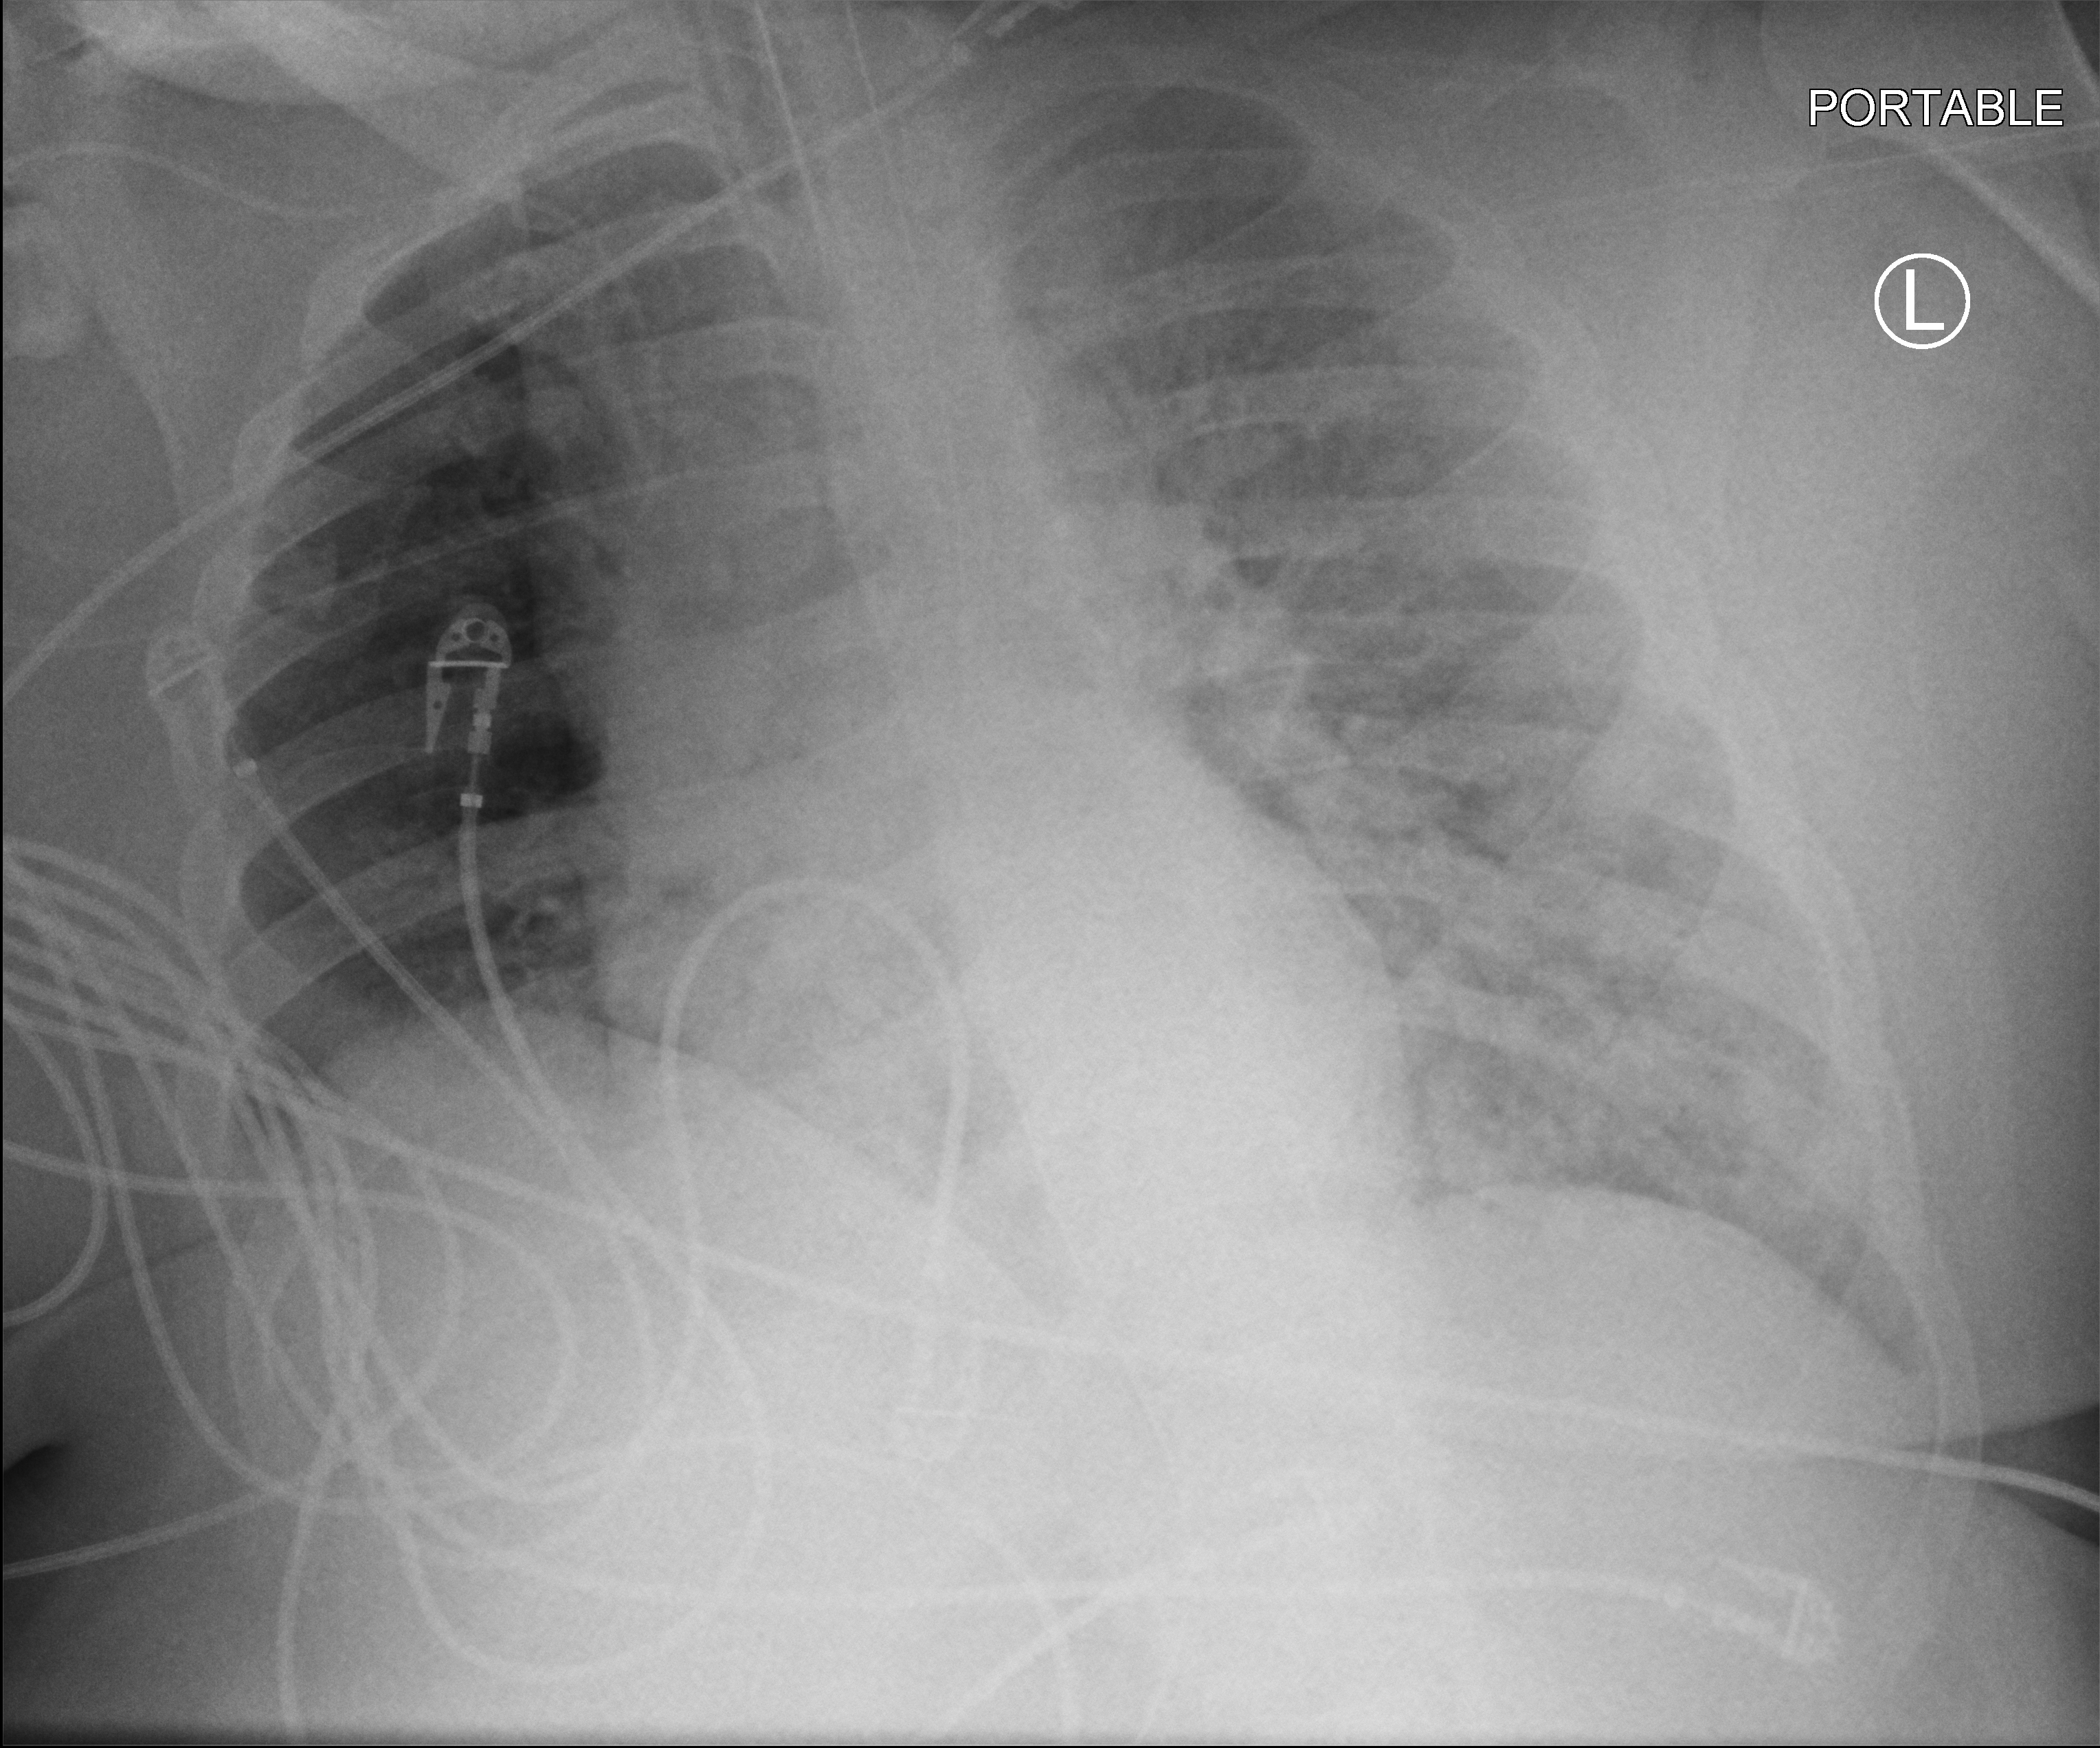
Portable chest radiograph, anteroposterior (AP) projection. Adult patient hospitalised with COVID-19, age 18–59 years.
Admission-level facts for this patient (not findings on this image; timing relative to this image not recorded):
- diabetes (admission record): yes
- admitted to intensive care during this hospital stay: yes